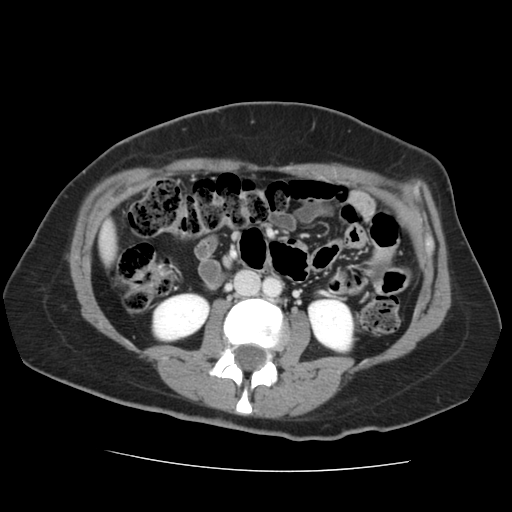
Contrast-enhanced abdominal CT, one axial slice. Position 40 of 144 along the scan axis. 120 kVp. Intravenous contrast given. Soft-tissue window (W 400 / L 40 HU). 512 × 512 image matrix, field of view 333 × 333 mm. Female patient, age 46 years. Case-level facts recorded for this patient, not image findings: diagnosis: colorectal cancer liver metastases, imaged before liver resection; multiple liver metastases: no; largest metastasis: 2.8 cm; disease in both lobes: no.
Annotated regions visible in this slice (outlined manually by an expert reader):
- liver: bounding box <102,227,115,259> (left, top, right, bottom; pixels)